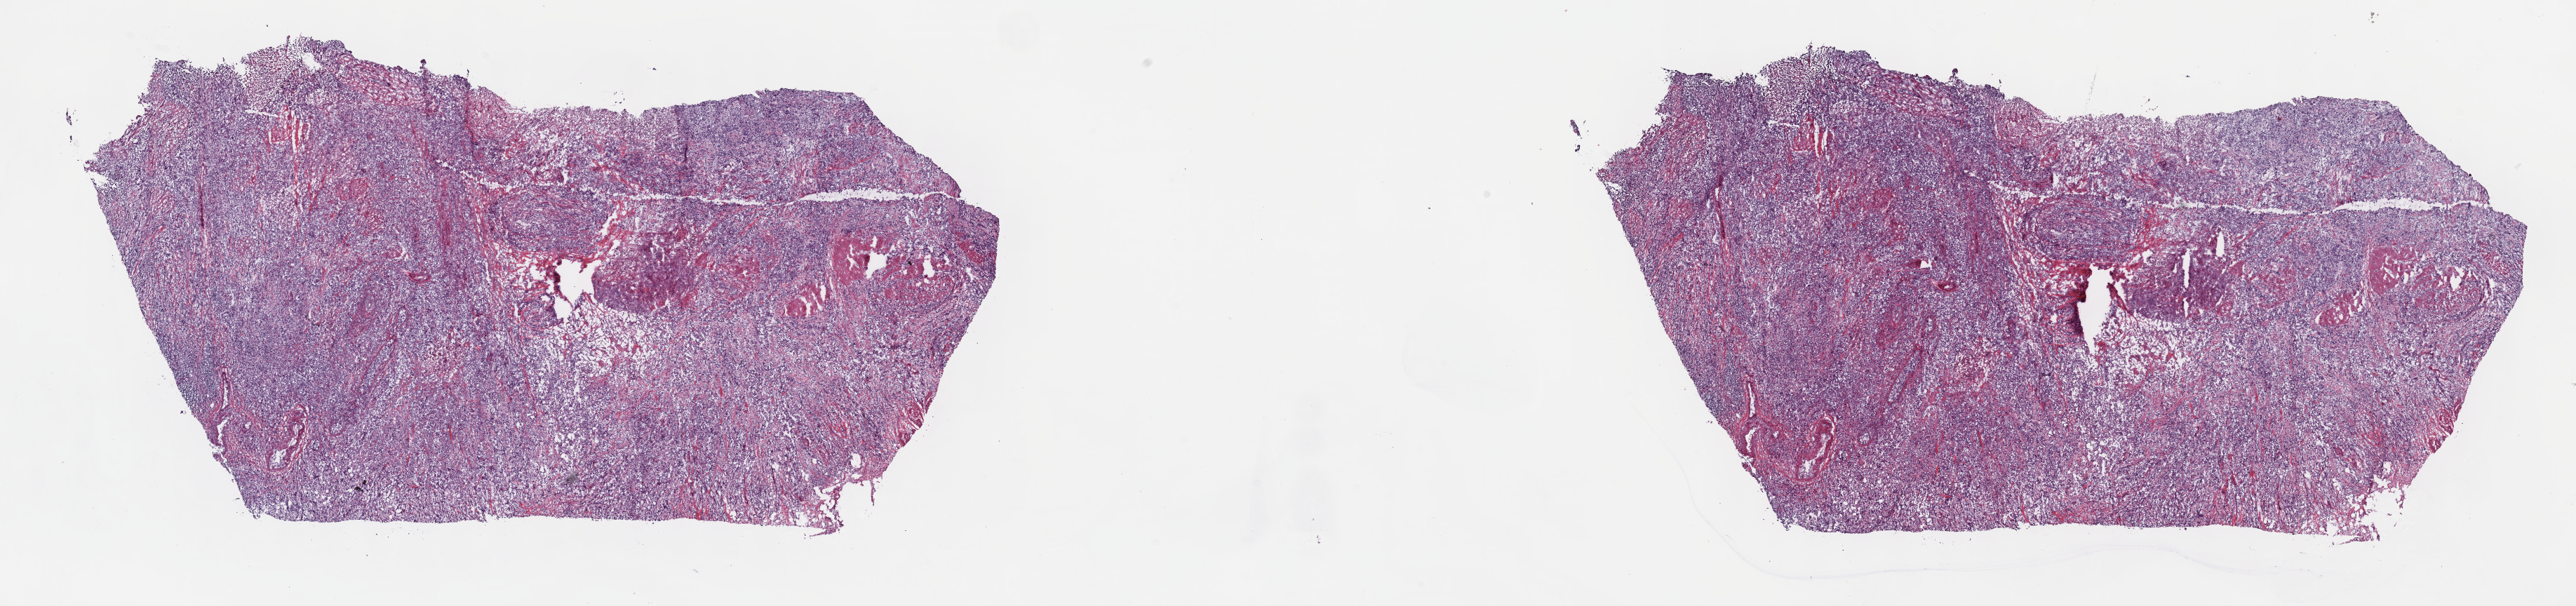
Digitized Hematoxylin and eosin (H&E) stained tissue section (whole slide), shown as a low-resolution overview of the whole scanned area (about 29.7 x 7.0 mm, acquisition: 40x scan); frozen section from the top of the tissue portion; bladder, primary tumour sample. Male patient; age at initial diagnosis 48 years.
Histologic diagnosis: Transitional cell carcinoma (lateral wall of bladder).